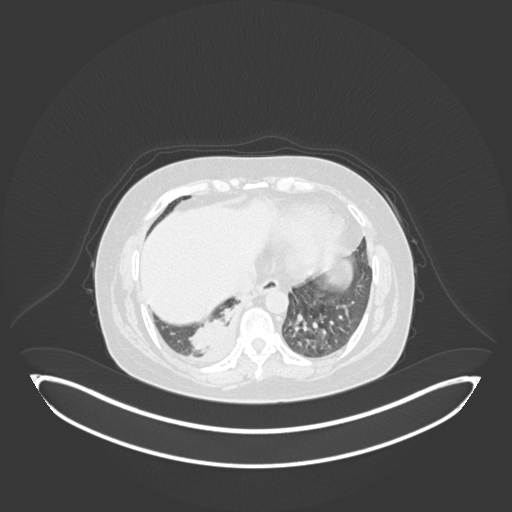
Chest CT, one axial slice. Slice 33 of 231 in the series (ordered by position). Reconstruction kernel B30f. Lung window (W 1500 / L -600 HU). 1 mm slice thickness. 512 × 512 image matrix, field of view 500 × 500 mm. Female patient, age 56 years. From the clinical record (not read from this slice): clinical TNM (as recorded): T2b N1 M0.
Outlined on this slice (rectangle marked by the reading radiologist):
- lung tumour (recorded histology: small cell carcinoma): box from (x=187, y=300) to (x=232, y=355) px